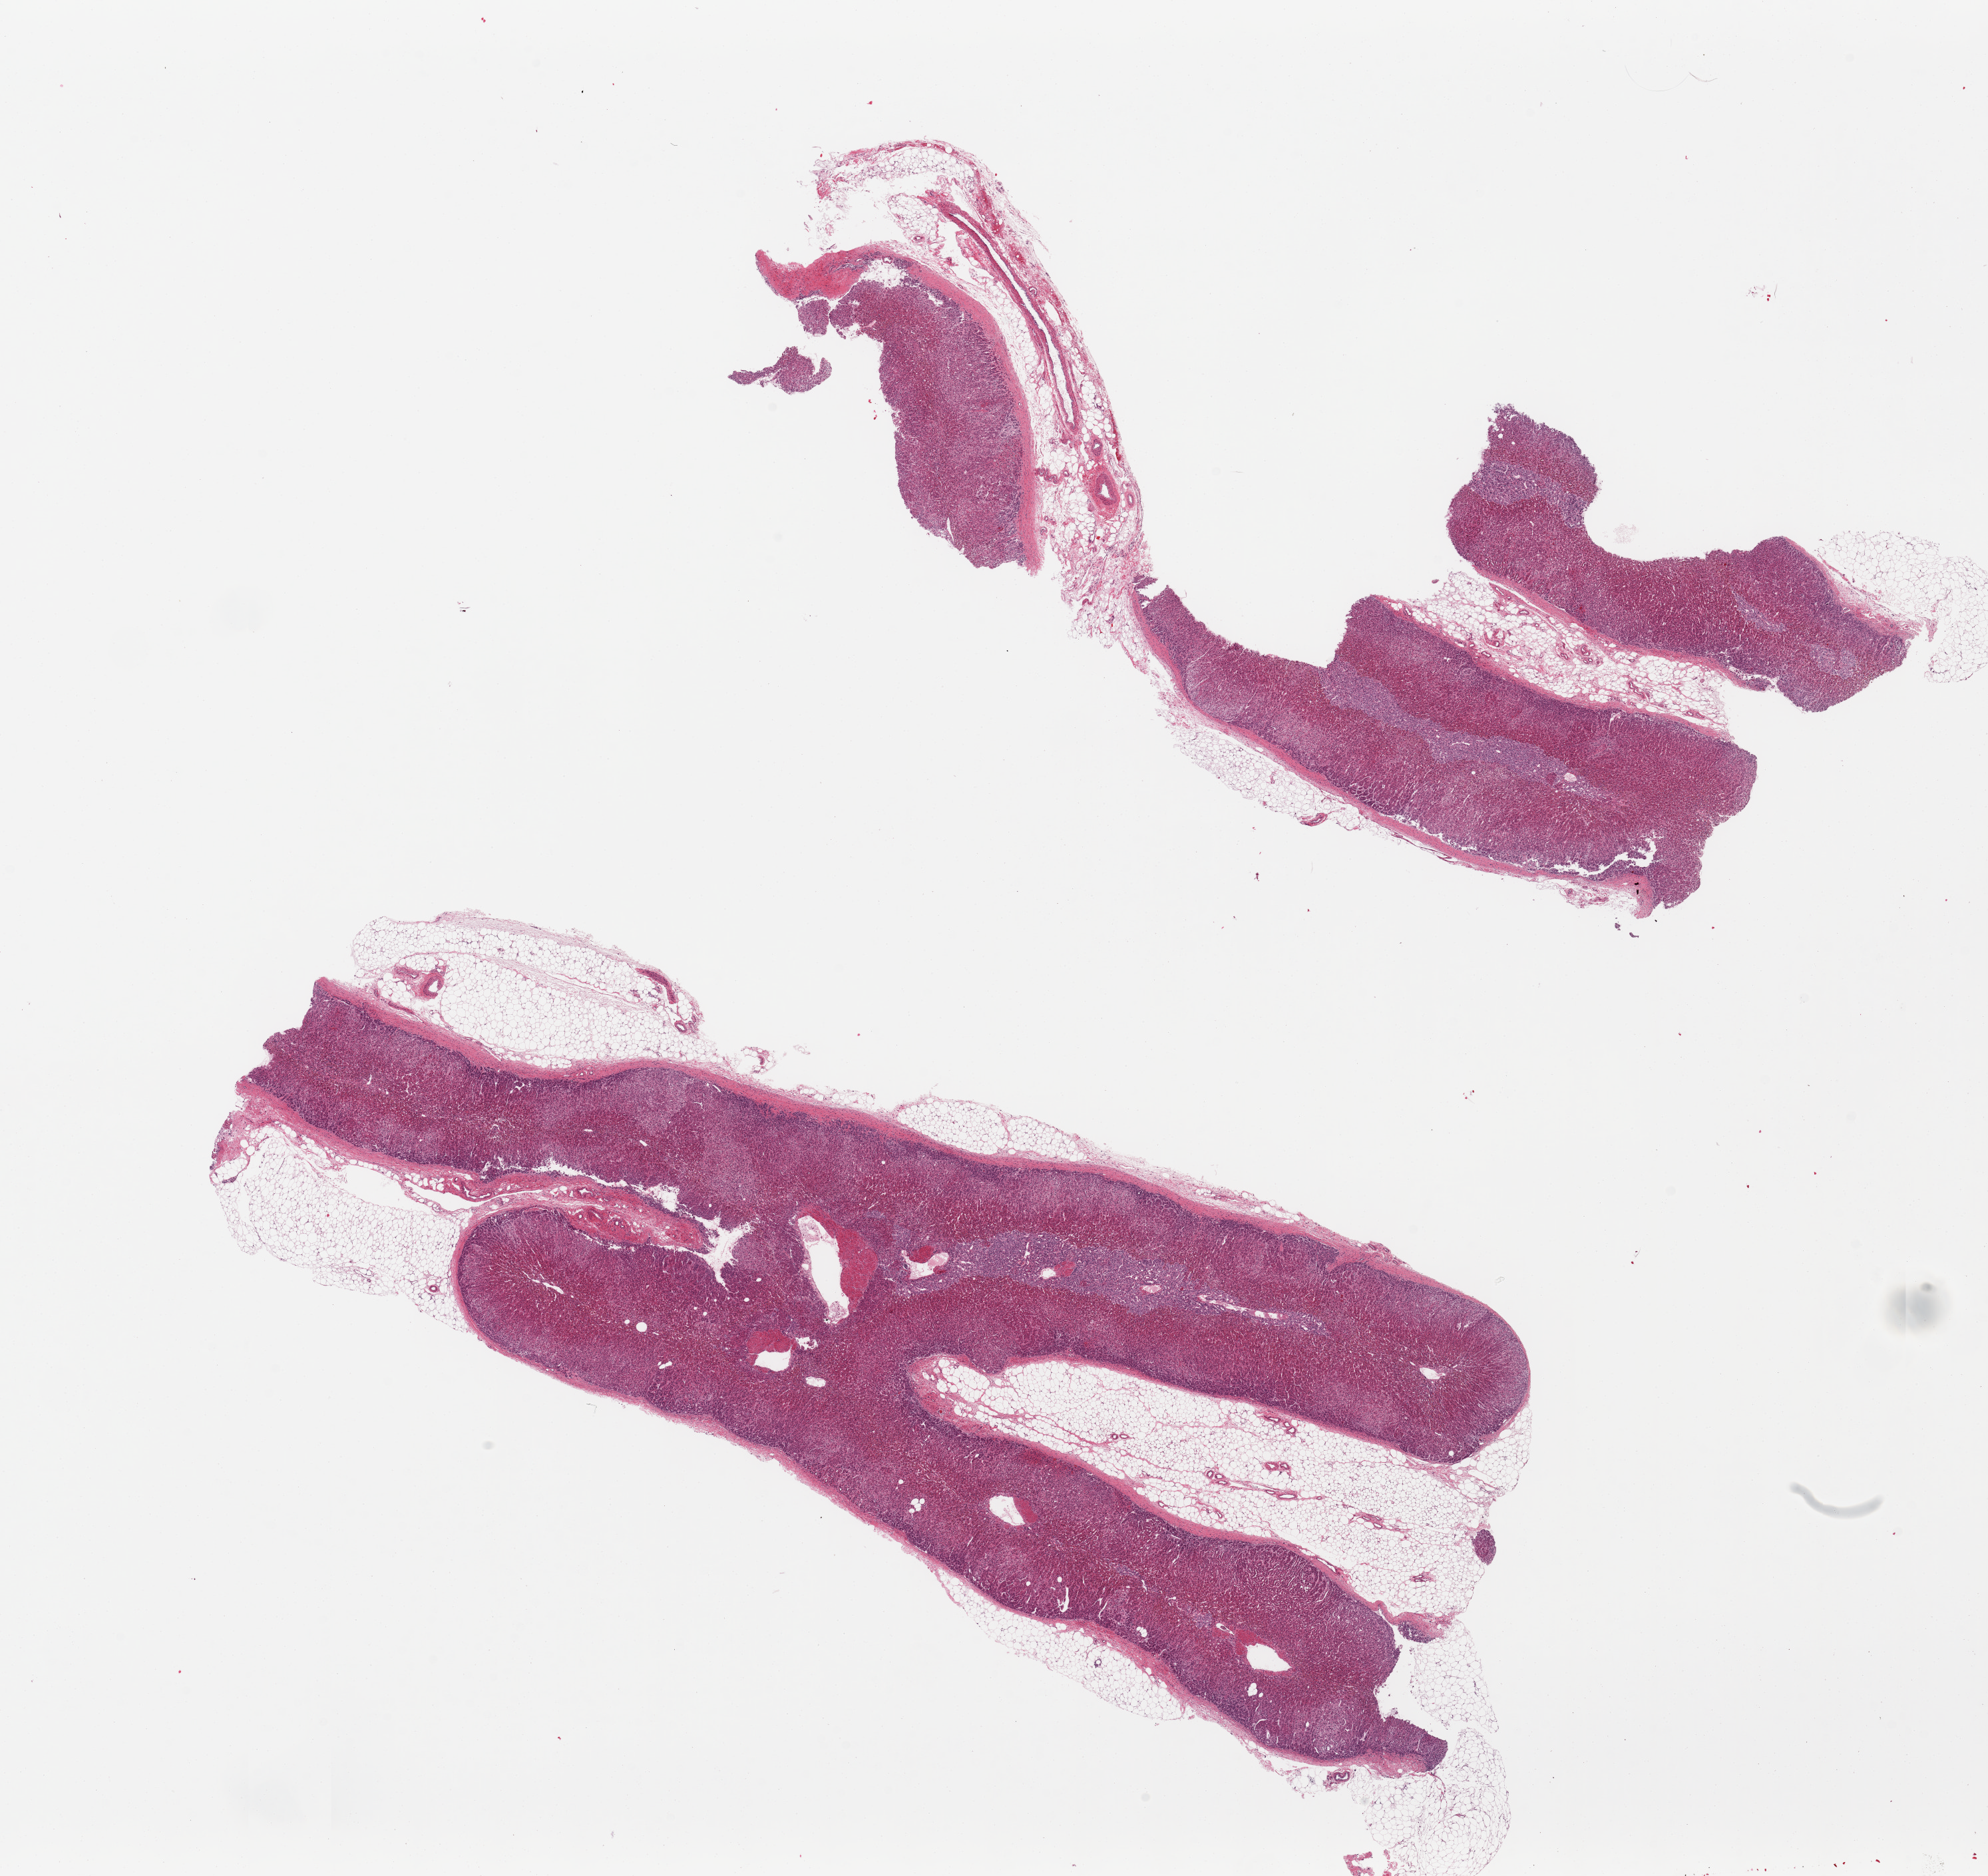
H&E whole-slide image, low-resolution overview of the scanned area, about 23.6 x 22.3 mm, PAXgene-fixed, paraffin-embedded tissue, target tissue: adrenal gland, tissue donor sample. Donor sex: female.
Reviewer comment on this tissue sample: 2 pieces, cortex and medulla; ~40% adherent/intermingled fat with dotted line.